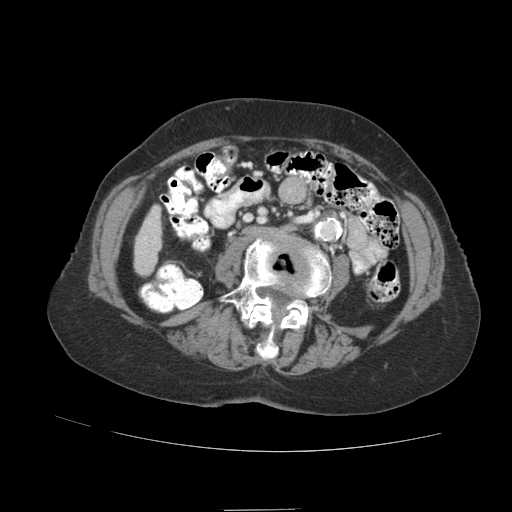
Contrast-enhanced abdominal CT (liver protocol), one axial slice; position 11 of 89 along the scan axis; reconstruction kernel STANDARD; soft-tissue window (W 400 / L 40 HU); 2.5 mm slice thickness; 512 × 512 image matrix, field of view 360 × 360 mm. From the clinical record (not read from this slice): diagnosis: hepatocellular carcinoma (patient treated with transarterial chemoembolisation; whether this scan precedes or follows treatment is not stated here); TNM stage (as recorded): Stage-II; Child-Pugh class: A; tumour size: 4 cm.
Structures marked on this image (semi-automatic segmentation, software-assisted and operator-edited):
- liver parenchyma outside the tumour (the mass and vessels are separate outlines, so this box may not span the whole liver): bounding box <134,206,162,276> (left, top, right, bottom; pixels)